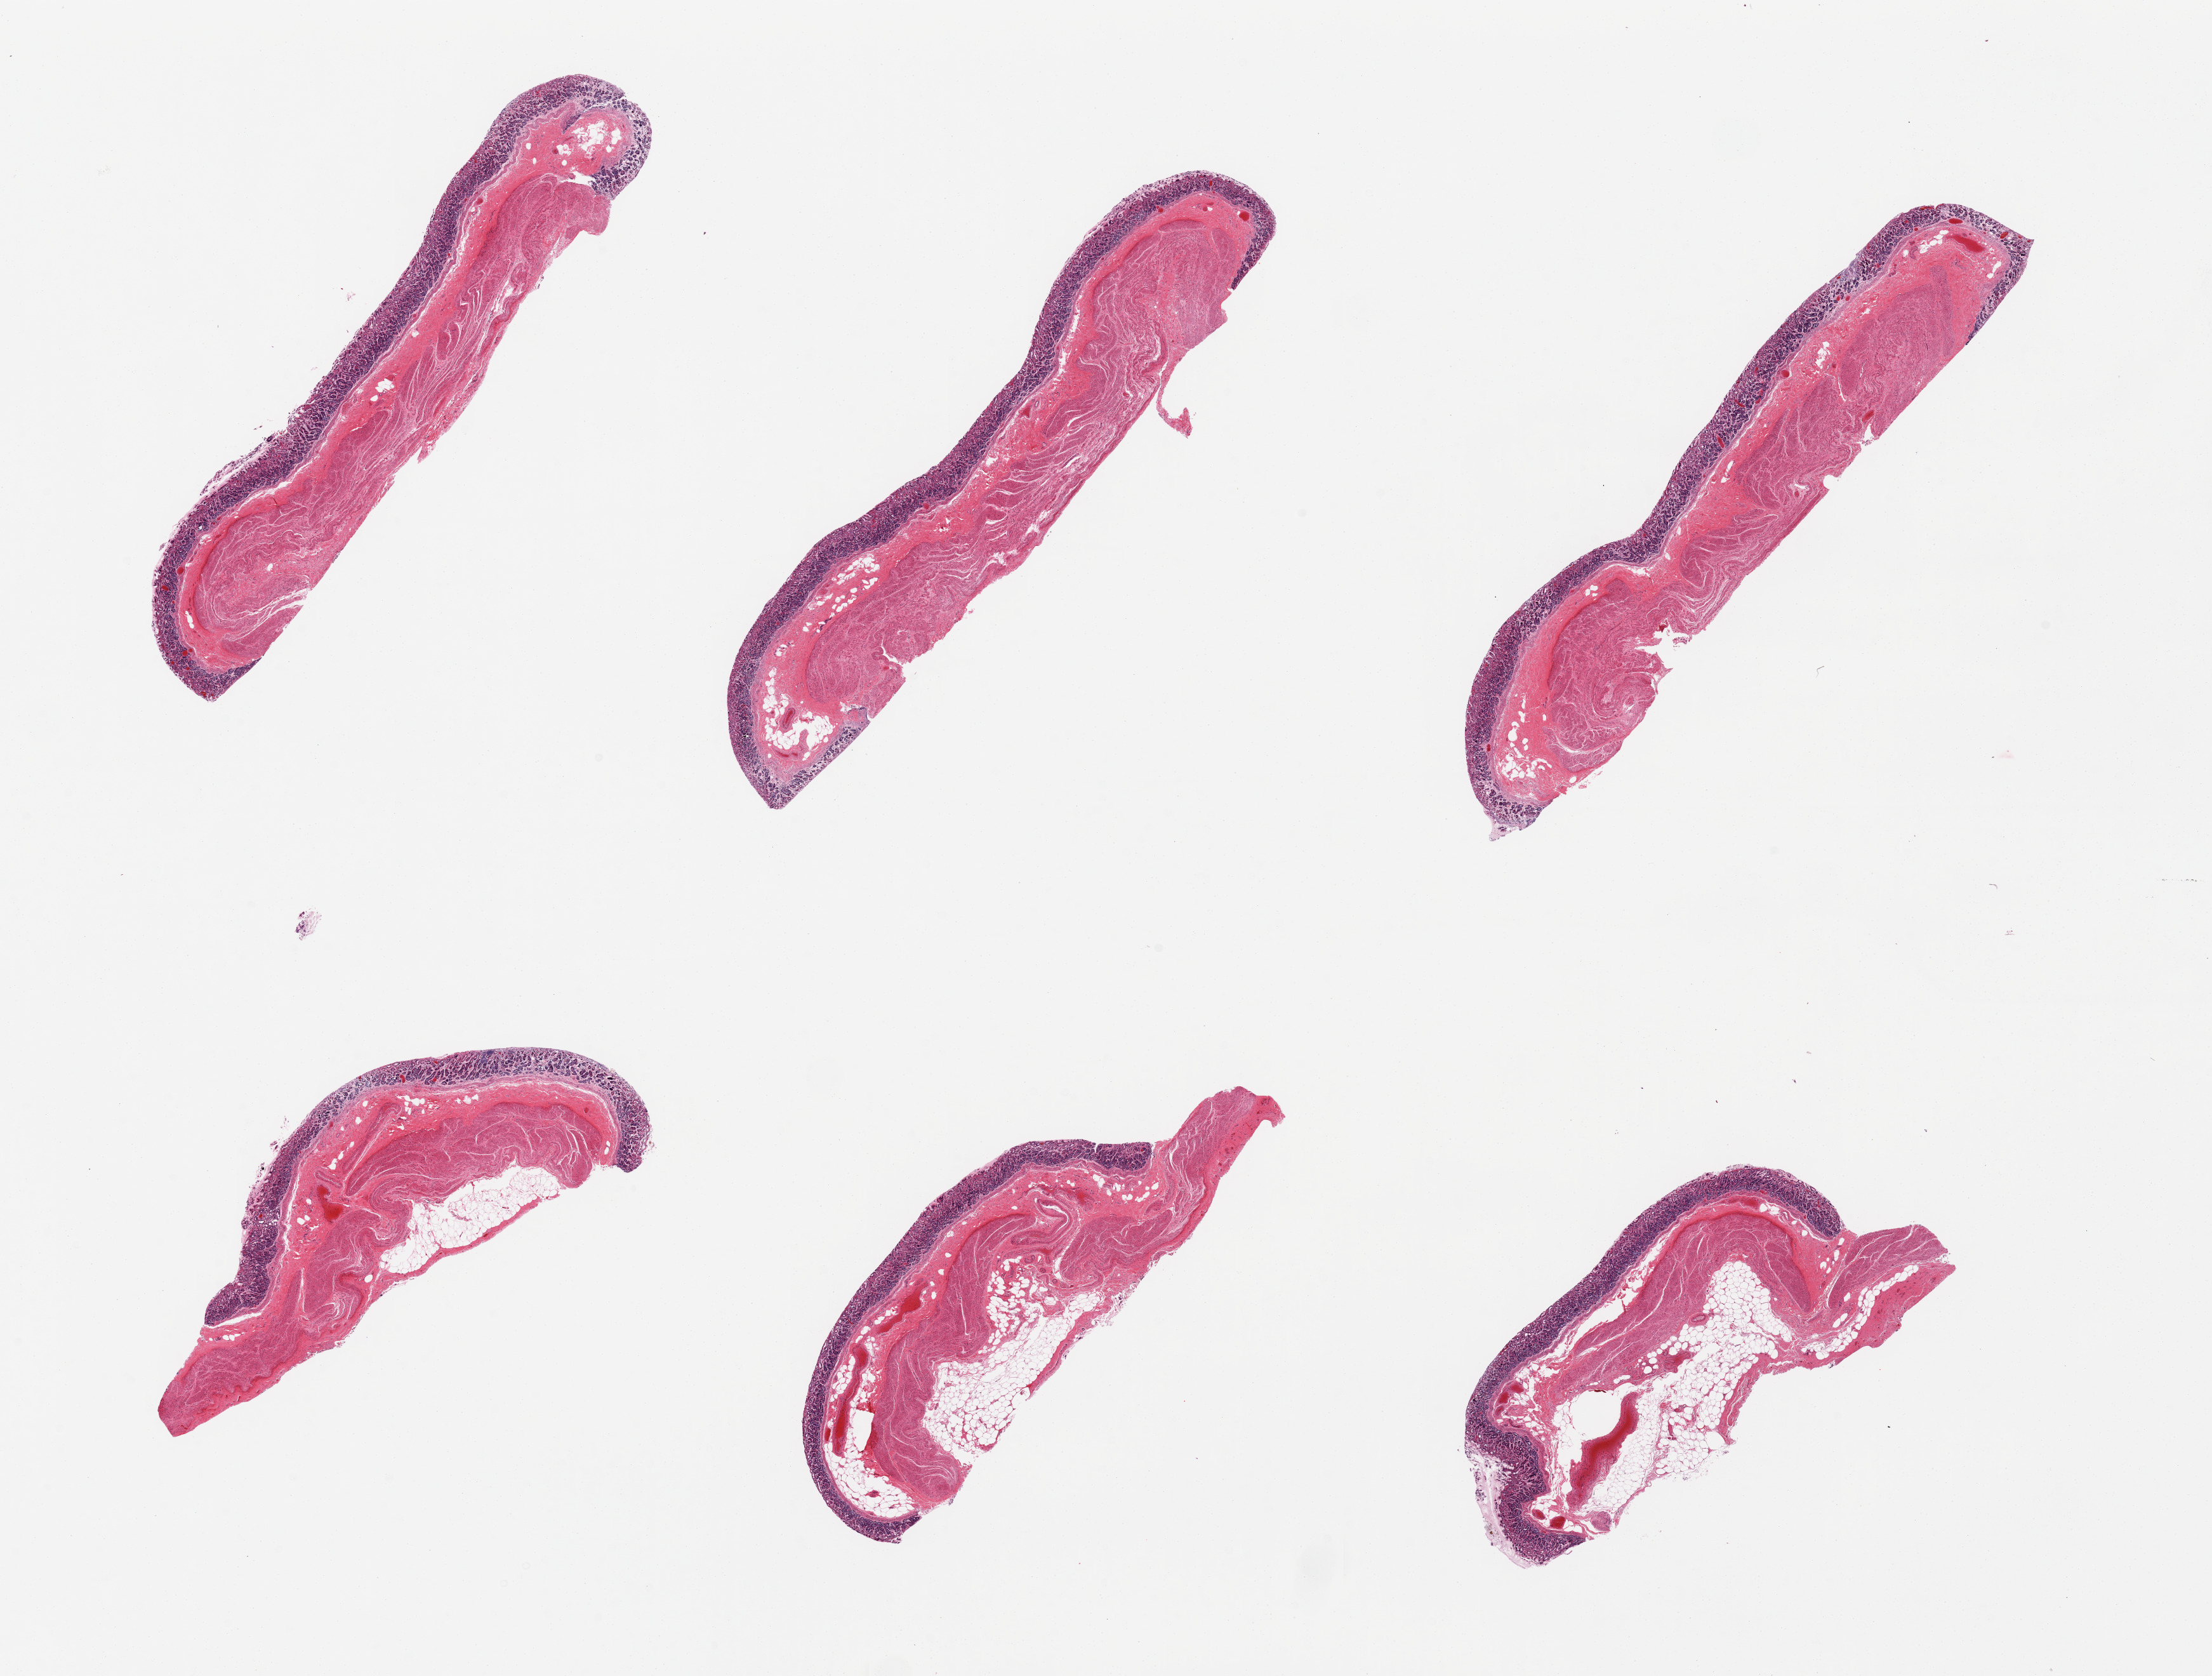
Digitized hematoxylin and eosin (H&E)-stained section — shown as a low-resolution overview of the whole scanned area (about 27.6 x 20.9 mm, from a 20x scan). PAXgene-fixed paraffin-embedded (PFPE) section. Section of stomach (target tissue). Tissue donor sample. Donor sex: male.
- review note (as recorded): 6 pieces, mucosa and muscularis